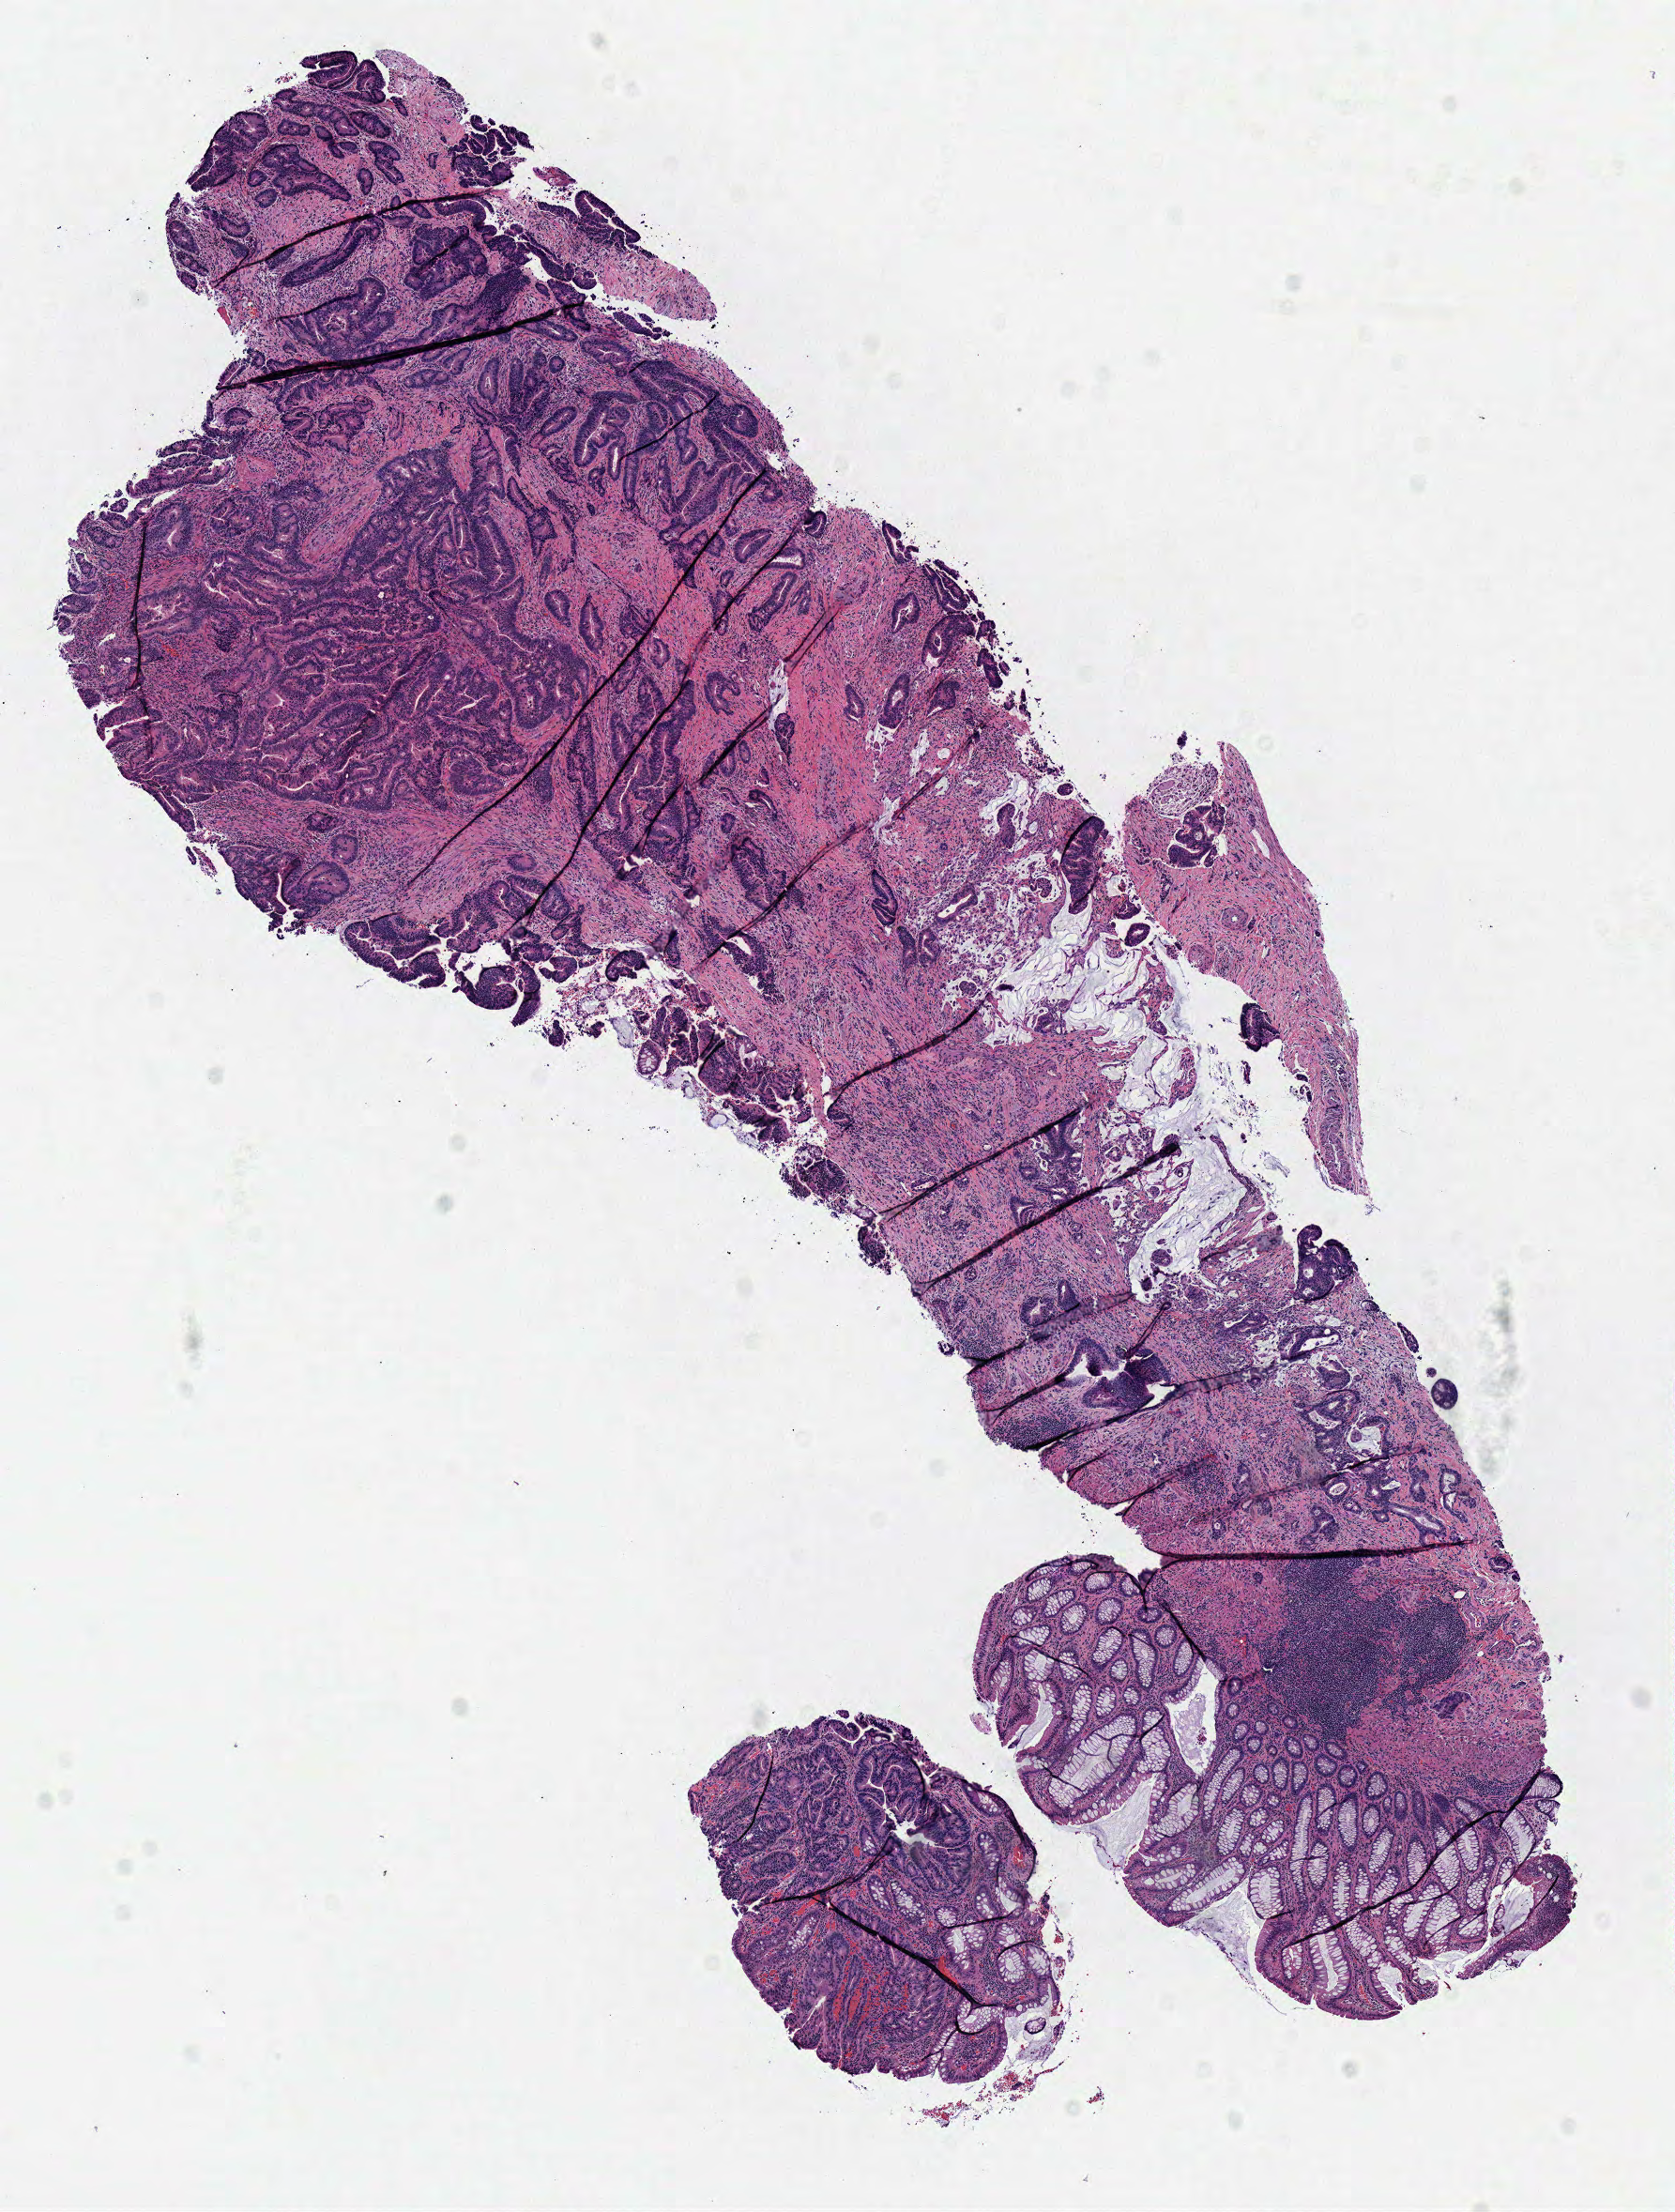
Digitized H&E-stained tissue section (whole slide), a low-resolution overview of the entire scanned area, about 7.0 x 9.3 mm (slide scanned at 40x); frozen section from the top of the tissue portion; sample: primary tumour, rectum. Patient: female, age at initial diagnosis 72 years. Composition of this section per pathologist review: tumour cells 83%, tumour nuclei 75%, normal cells 16%, stromal cells 0%, necrosis 1%. Inflammatory infiltration, as recorded: lymphocyte infiltration 15%, monocyte infiltration 0%, neutrophil infiltration 5%.
• AJCC pathologic stage: IIIB (7th edition)
• histologic diagnosis: Adenocarcinoma, NOS (rectosigmoid junction)
• lymph nodes positive (case pathology): 2 of 52 examined